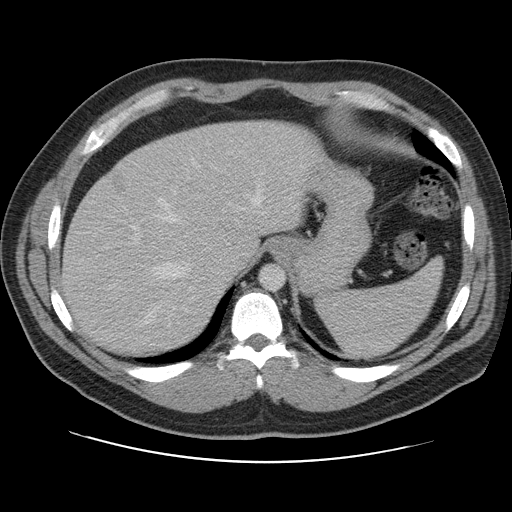
Contrast-enhanced abdominal CT, one axial slice; 120 kVp; intravenous contrast given; soft-tissue window (W 400 / L 40 HU); 512 × 512 image matrix, field of view 402 × 402 mm. Male patient, age 35 years. From the clinical record (not read from this slice): diagnosis: colorectal cancer liver metastases, imaged before liver resection; multiple liver metastases: yes; largest metastasis: 2.8 cm; disease in both lobes: yes.
Structures marked on this image (expert manual segmentation):
- hepatic veins: bounding box <144,183,264,326> (left, top, right, bottom; pixels)
- liver: <63,121,314,355>
- planned liver remnant (the part of the liver to remain after resection): <63,121,310,355>
- portal vein (with intrahepatic branches): <120,160,220,270>
- liver metastasis: <115,177,121,186>